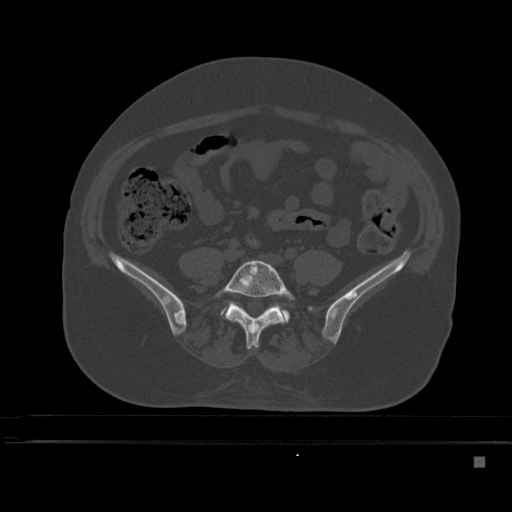
CT including the spine, one axial slice; slice 108 of 495 in the series (ordered by position); bone window (W 1800 / L 400 HU); 512 × 512 image matrix, field of view 404 × 404 mm. Female patient, age 33 years. From the clinical record (not read from this slice): primary cancer: breast.
Annotated regions visible in this slice (semi-automatic segmentation, software-assisted and operator-edited):
- L5 vertebra: bounding box [x1, y1, x2, y2] px = [214, 259, 295, 349]